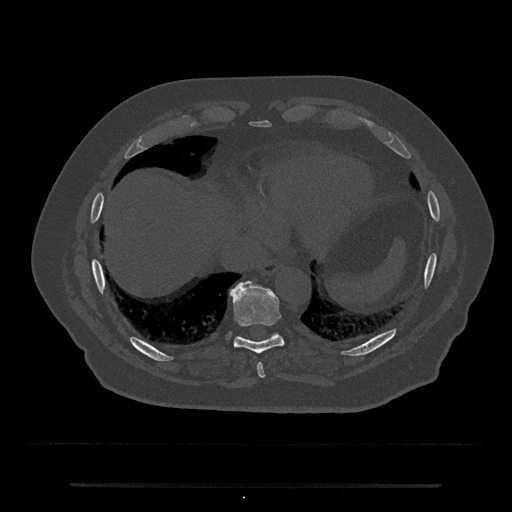
CT including the spine, one axial slice. Reconstruction kernel Br40s/3. Bone window (W 1800 / L 400 HU). 0.5 mm slice thickness. 512 × 512 image matrix. Patient: male, 80 years. Case-level facts recorded for this patient, not image findings: primary cancer: prostate; vertebrae with lytic lesions (as recorded): L1, T11.
Structures marked on this image (semi-automatic segmentation, software-assisted and operator-edited):
- T10 vertebra: bounding box [x1, y1, x2, y2] px = [237, 332, 279, 338]
- T8 vertebra: [257, 363, 265, 378]
- T9 vertebra: [230, 281, 284, 354]